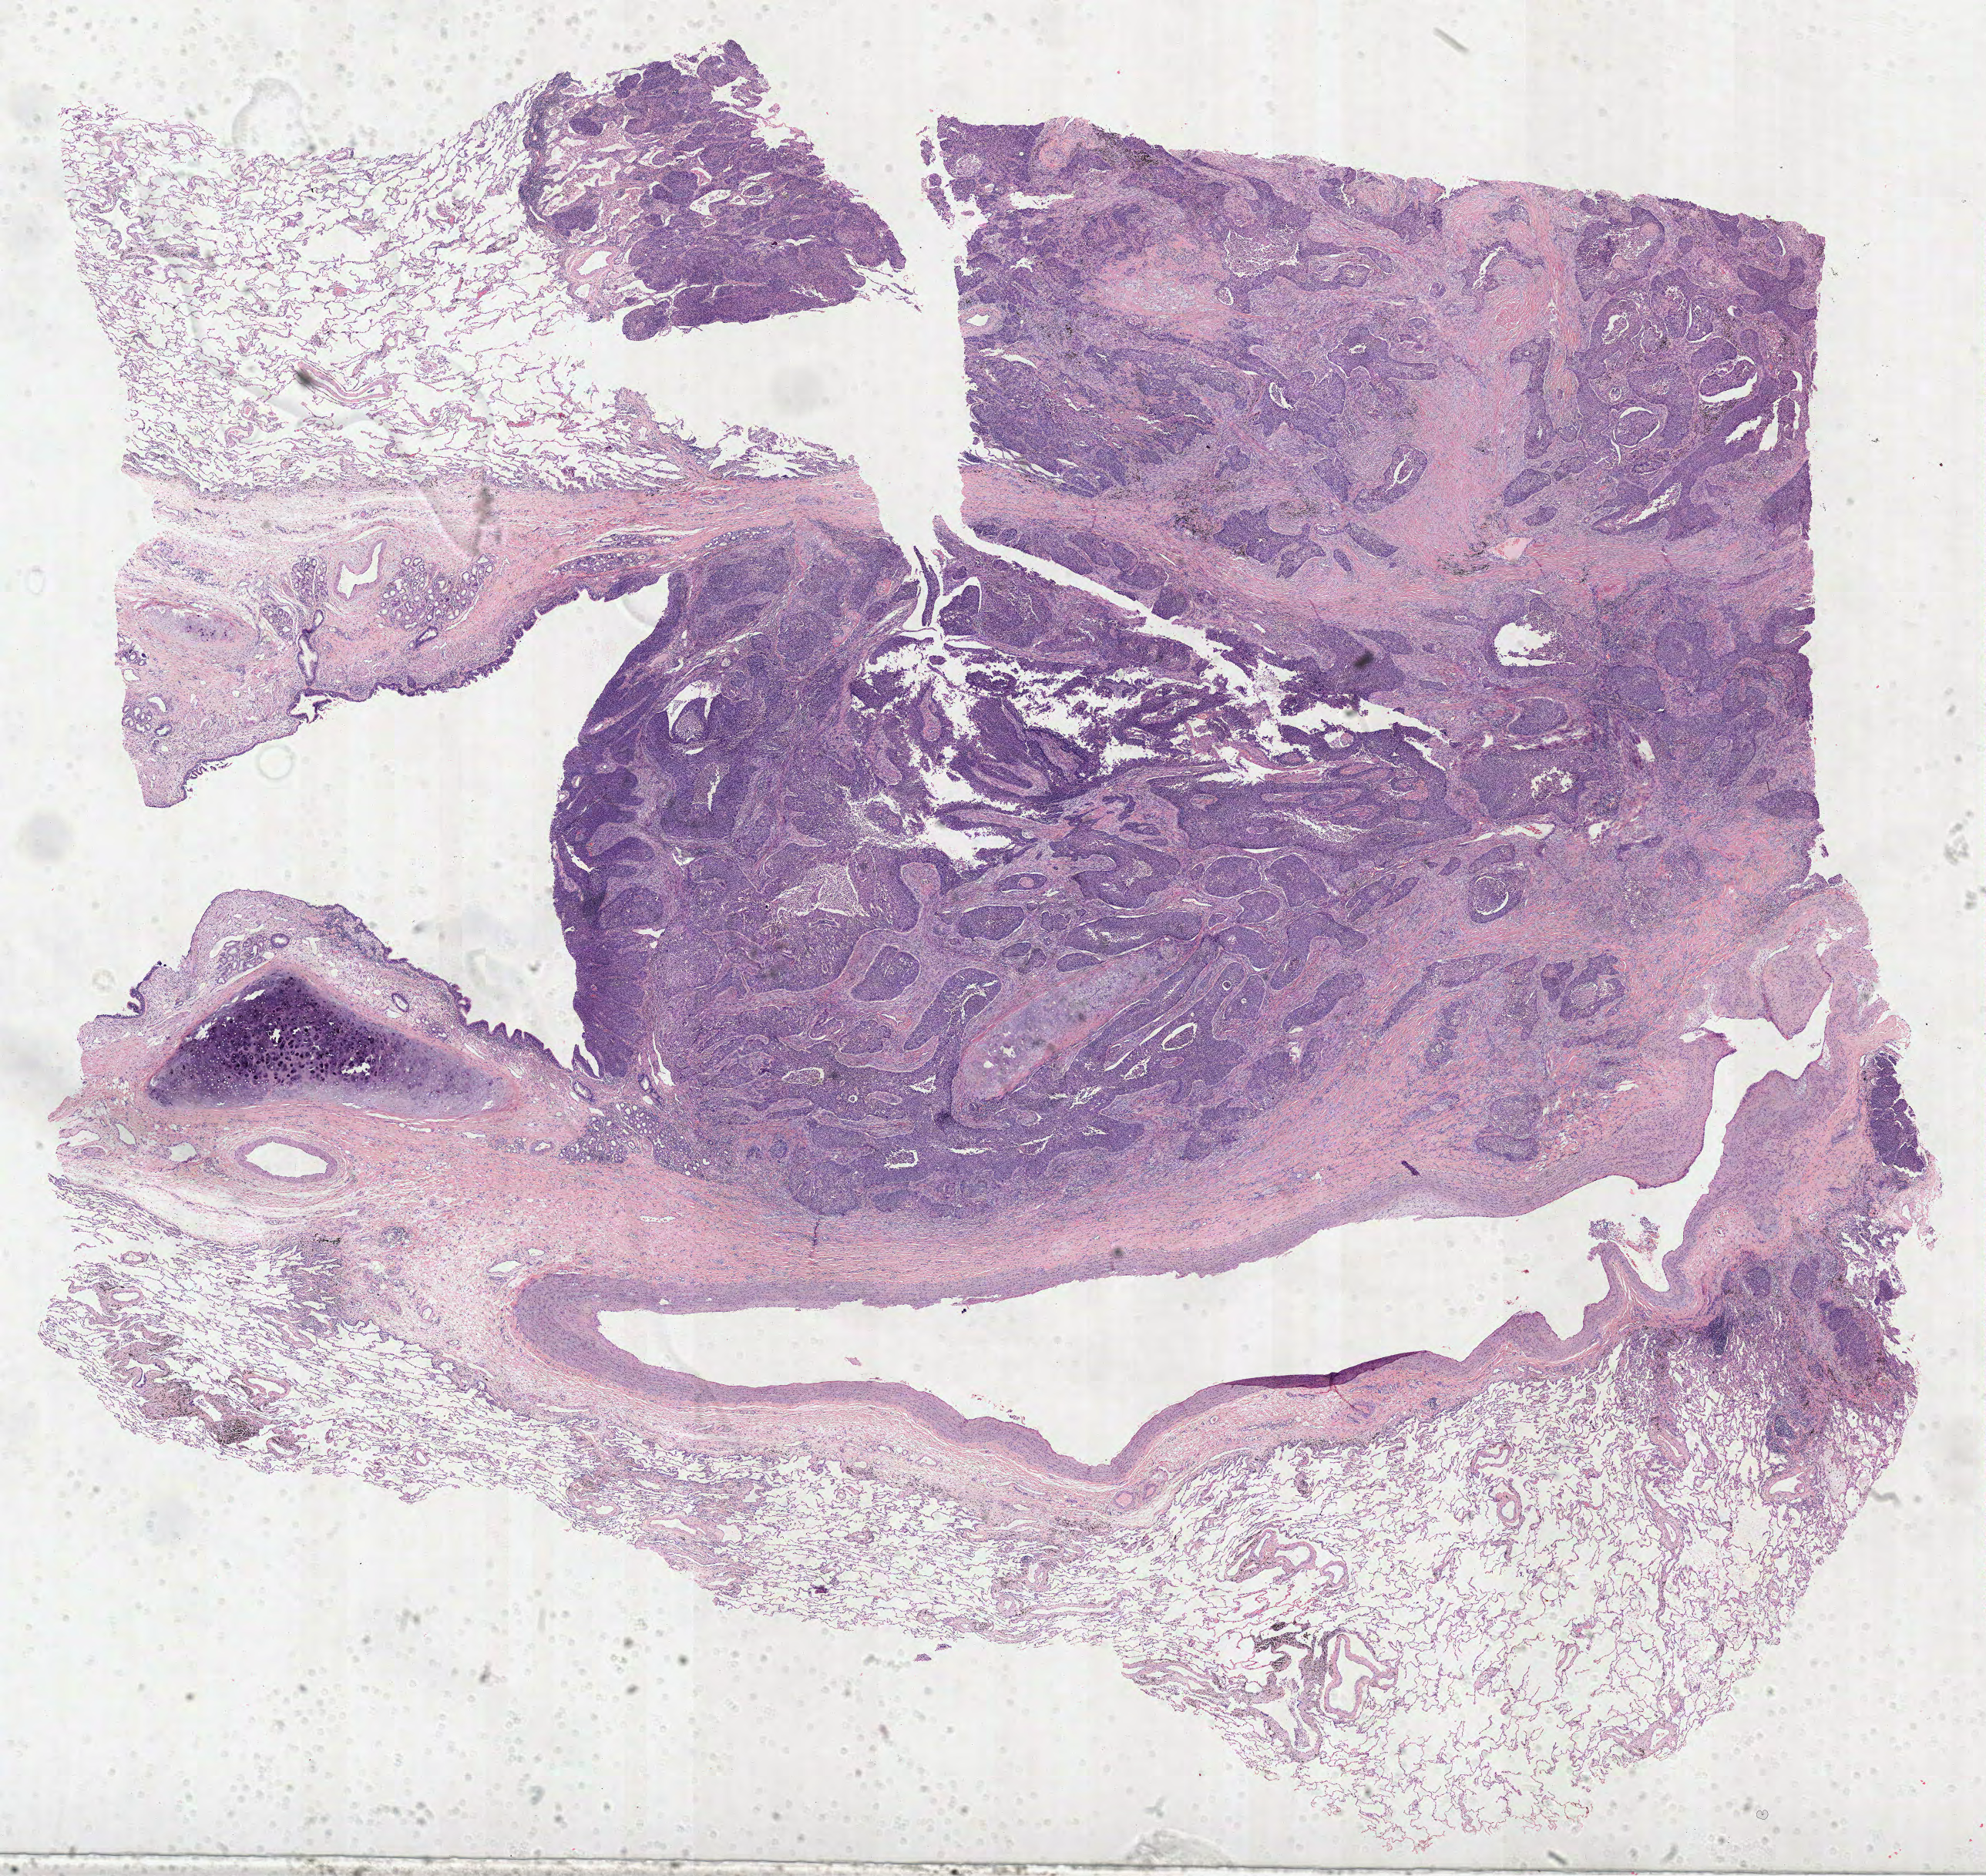
Hematoxylin and eosin (H&E) stained whole-slide image — shown as a low-resolution overview of the whole scanned area (about 20.8 x 19.6 mm). Formalin-fixed paraffin-embedded (FFPE) diagnostic section. Sample: primary tumour, lung. Patient: male, age at initial diagnosis 67 years.
AJCC pathologic stage: IA (6th edition). Pathologic diagnosis: Squamous cell carcinoma, NOS (lower lobe, lung). Laterality: right.